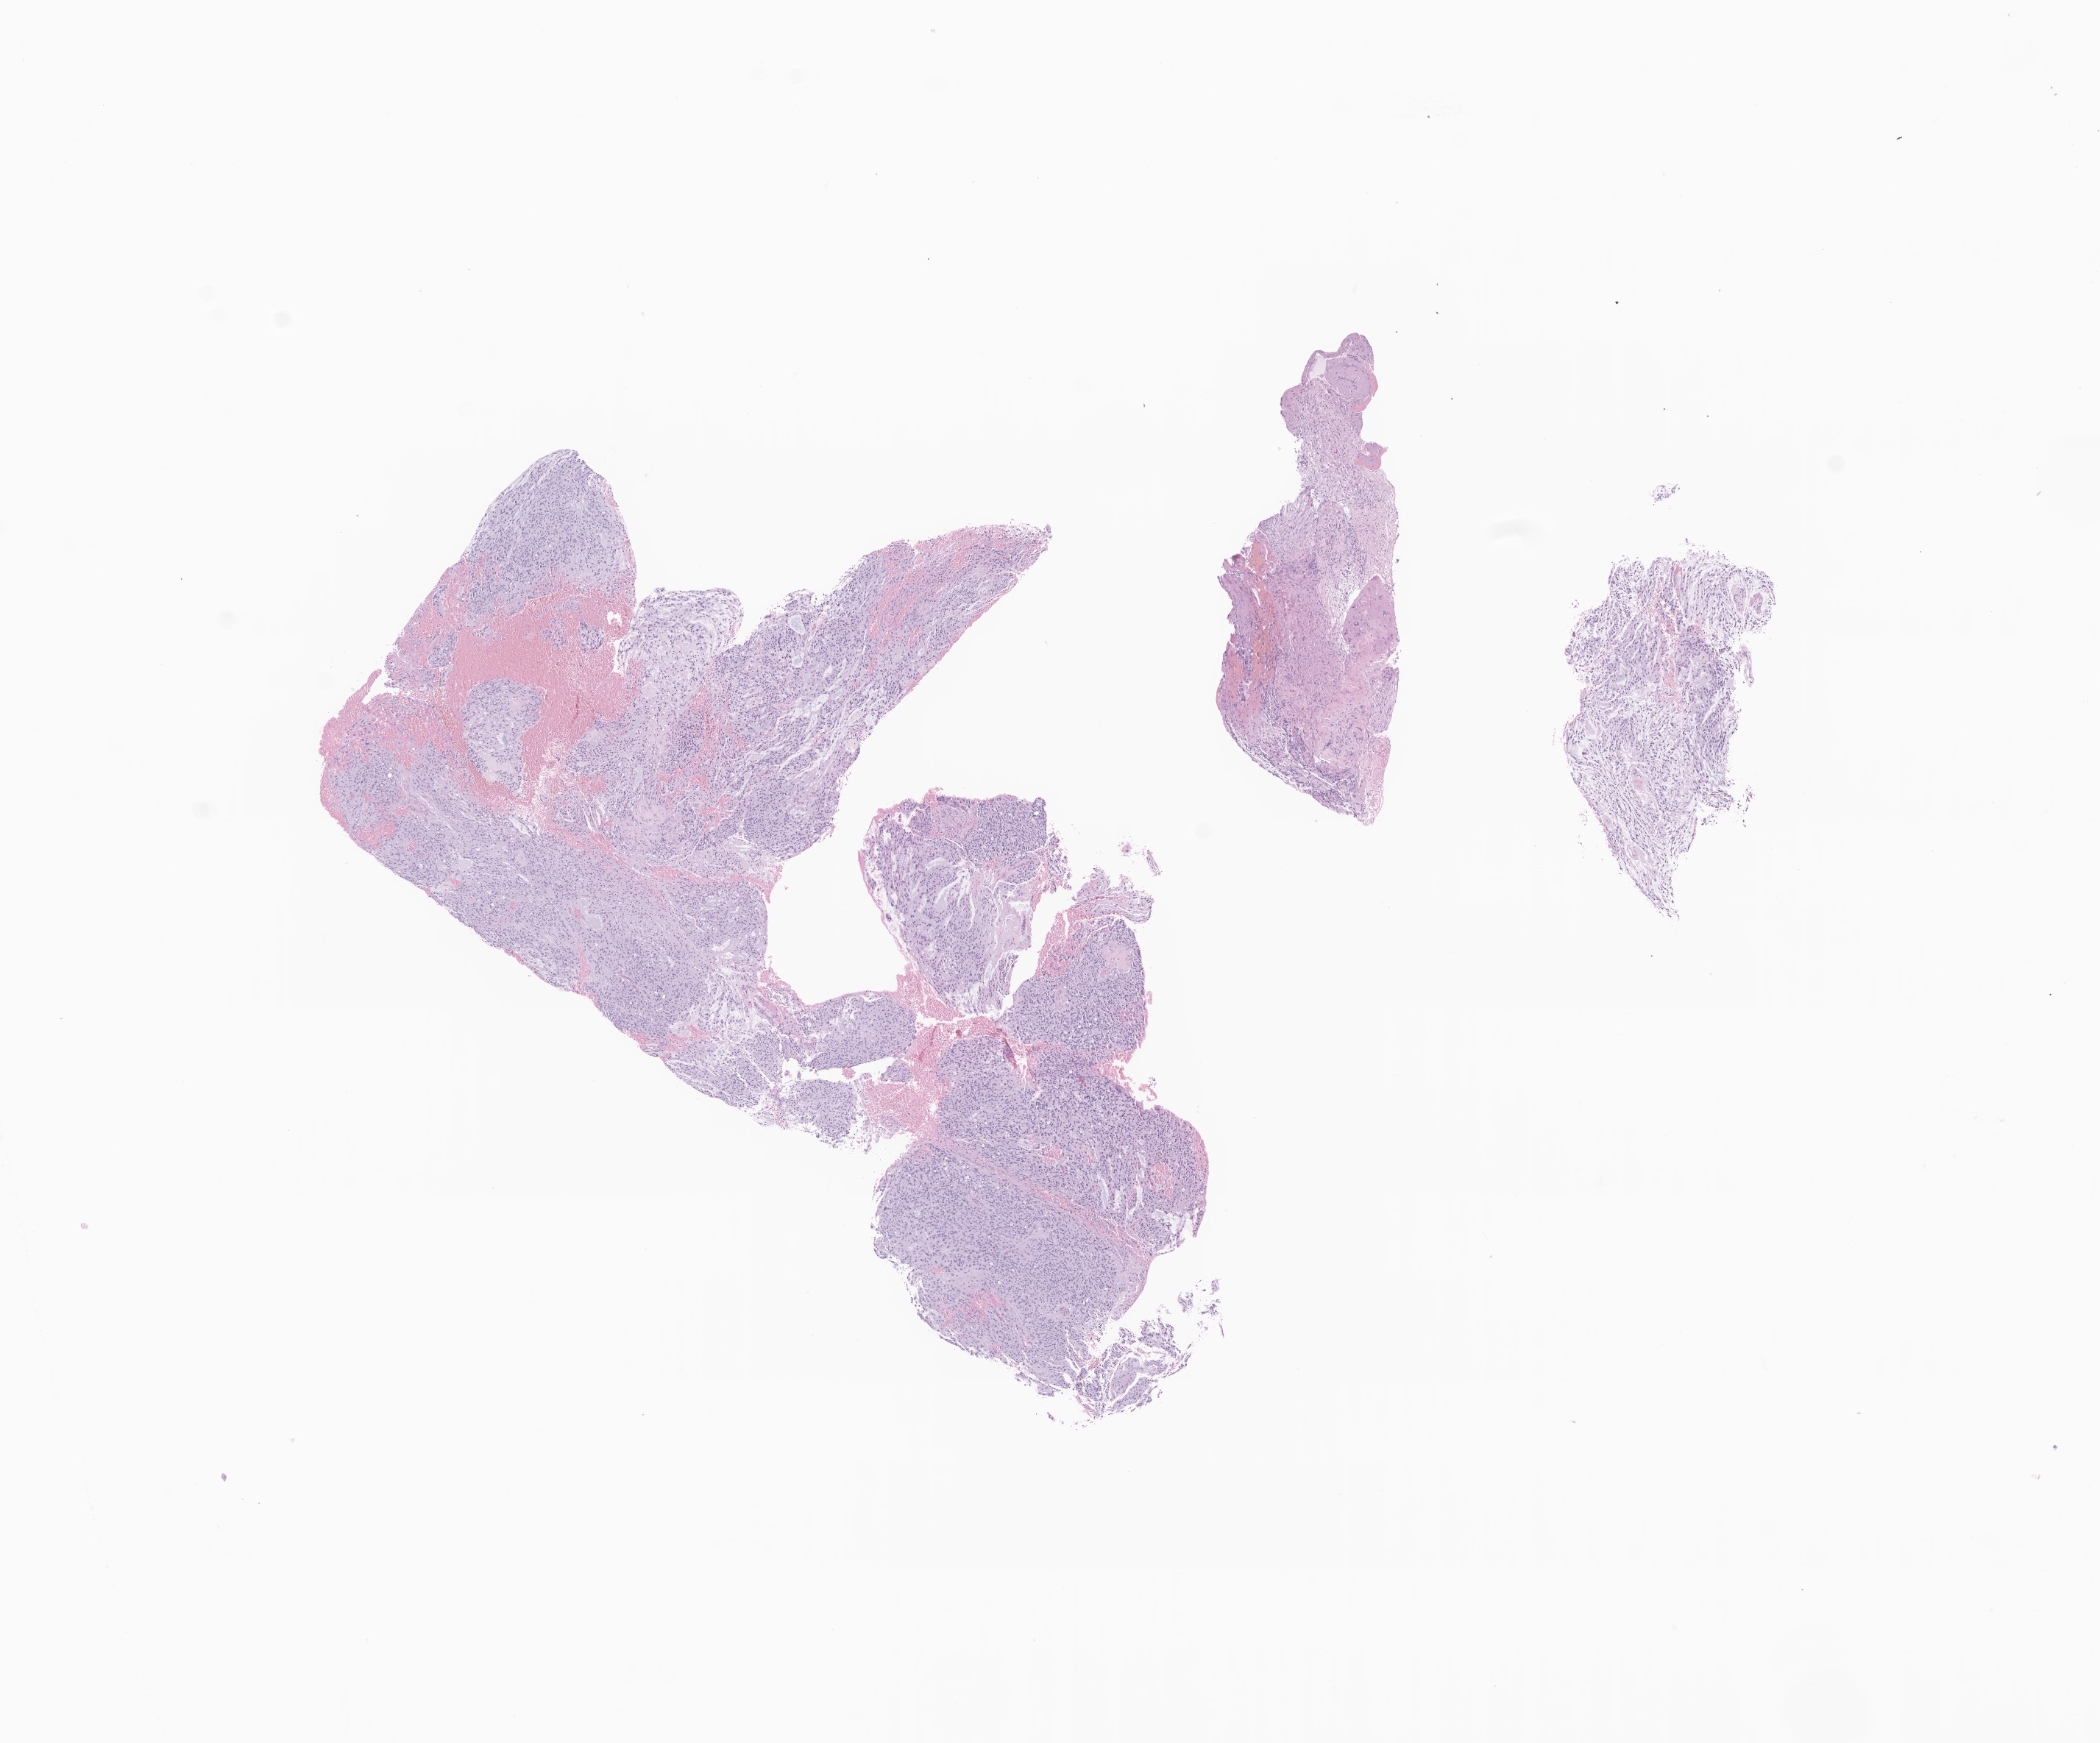
Digitized hematoxylin and eosin (H&E)-stained section of tumor tissue from the spinal cord — low-resolution overview of the scanned area, about 12.0 x 10.0 mm. Formalin-fixed paraffin-embedded section. Patient: male, age 75 months.
* diagnosis: Myxopapillary ependymoma